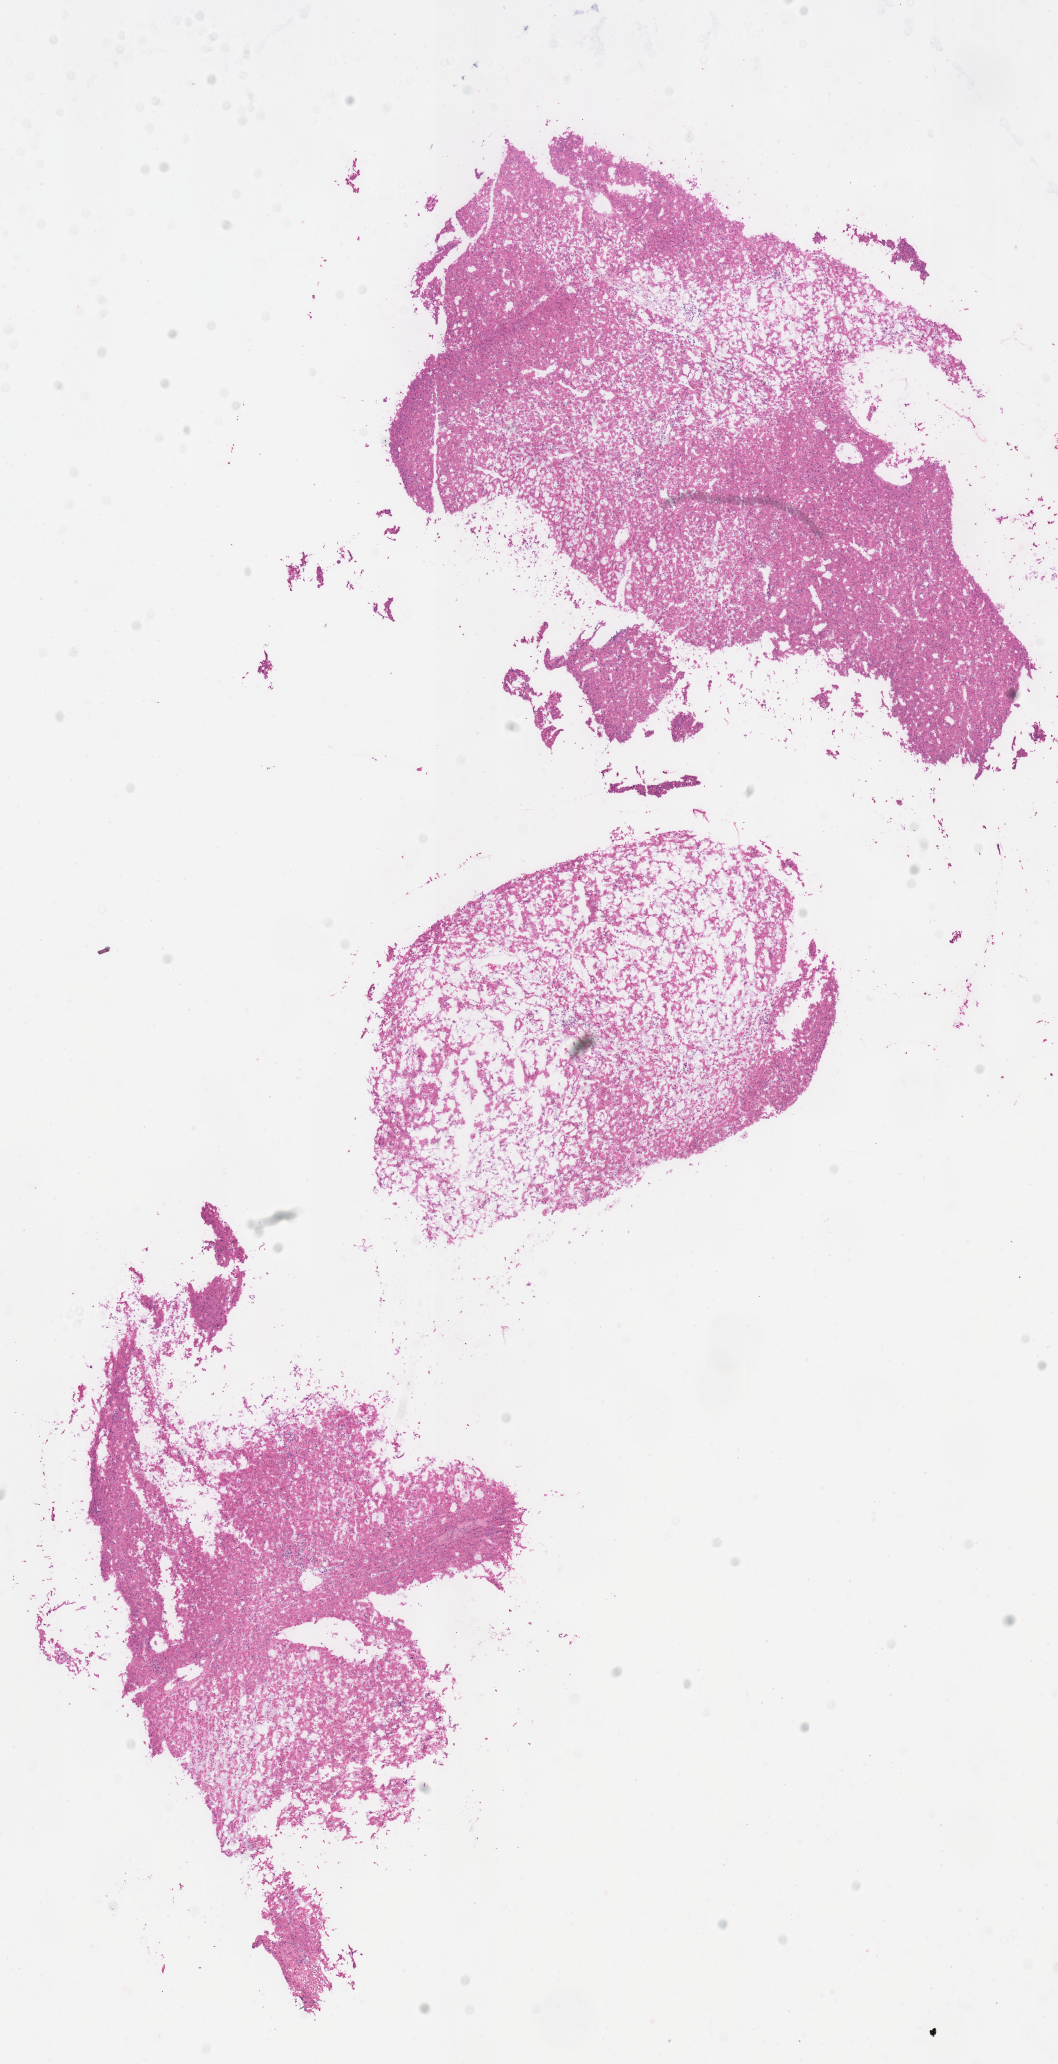
H&E-stained whole-slide image, a low-resolution overview of the entire scanned area, about 8.3 x 16.2 mm (acquisition: 40x scan), frozen section from the top of the tissue portion, sample: primary tumour, kidney. Female, age 61 years at initial diagnosis.
Diagnosis: Renal cell carcinoma, chromophobe type.